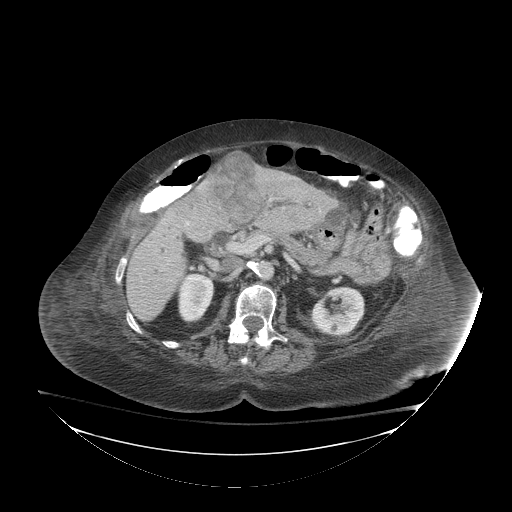
Contrast-enhanced abdominal CT (liver protocol), one axial slice; position 35 of 81 along the scan axis; reconstruction kernel STANDARD; 140 kVp; soft-tissue window (W 400 / L 40 HU); 2.5 mm slice thickness; 512 × 512 image matrix, field of view 500 × 500 mm. From the clinical record (not read from this slice): diagnosis: hepatocellular carcinoma (patient treated with transarterial chemoembolisation; whether this scan precedes or follows treatment is not stated here); TNM stage (as recorded): Stage-I; Child-Pugh class: B; tumour differentiation: well-moderately differentiated.
Annotated regions visible in this slice (semi-automatically segmented with operator editing):
- liver parenchyma outside the tumour (the mass and vessels are separate outlines, so this box may not span the whole liver): bounding box <124,172,334,320> (left, top, right, bottom; pixels)
- mass: <201,150,261,222>